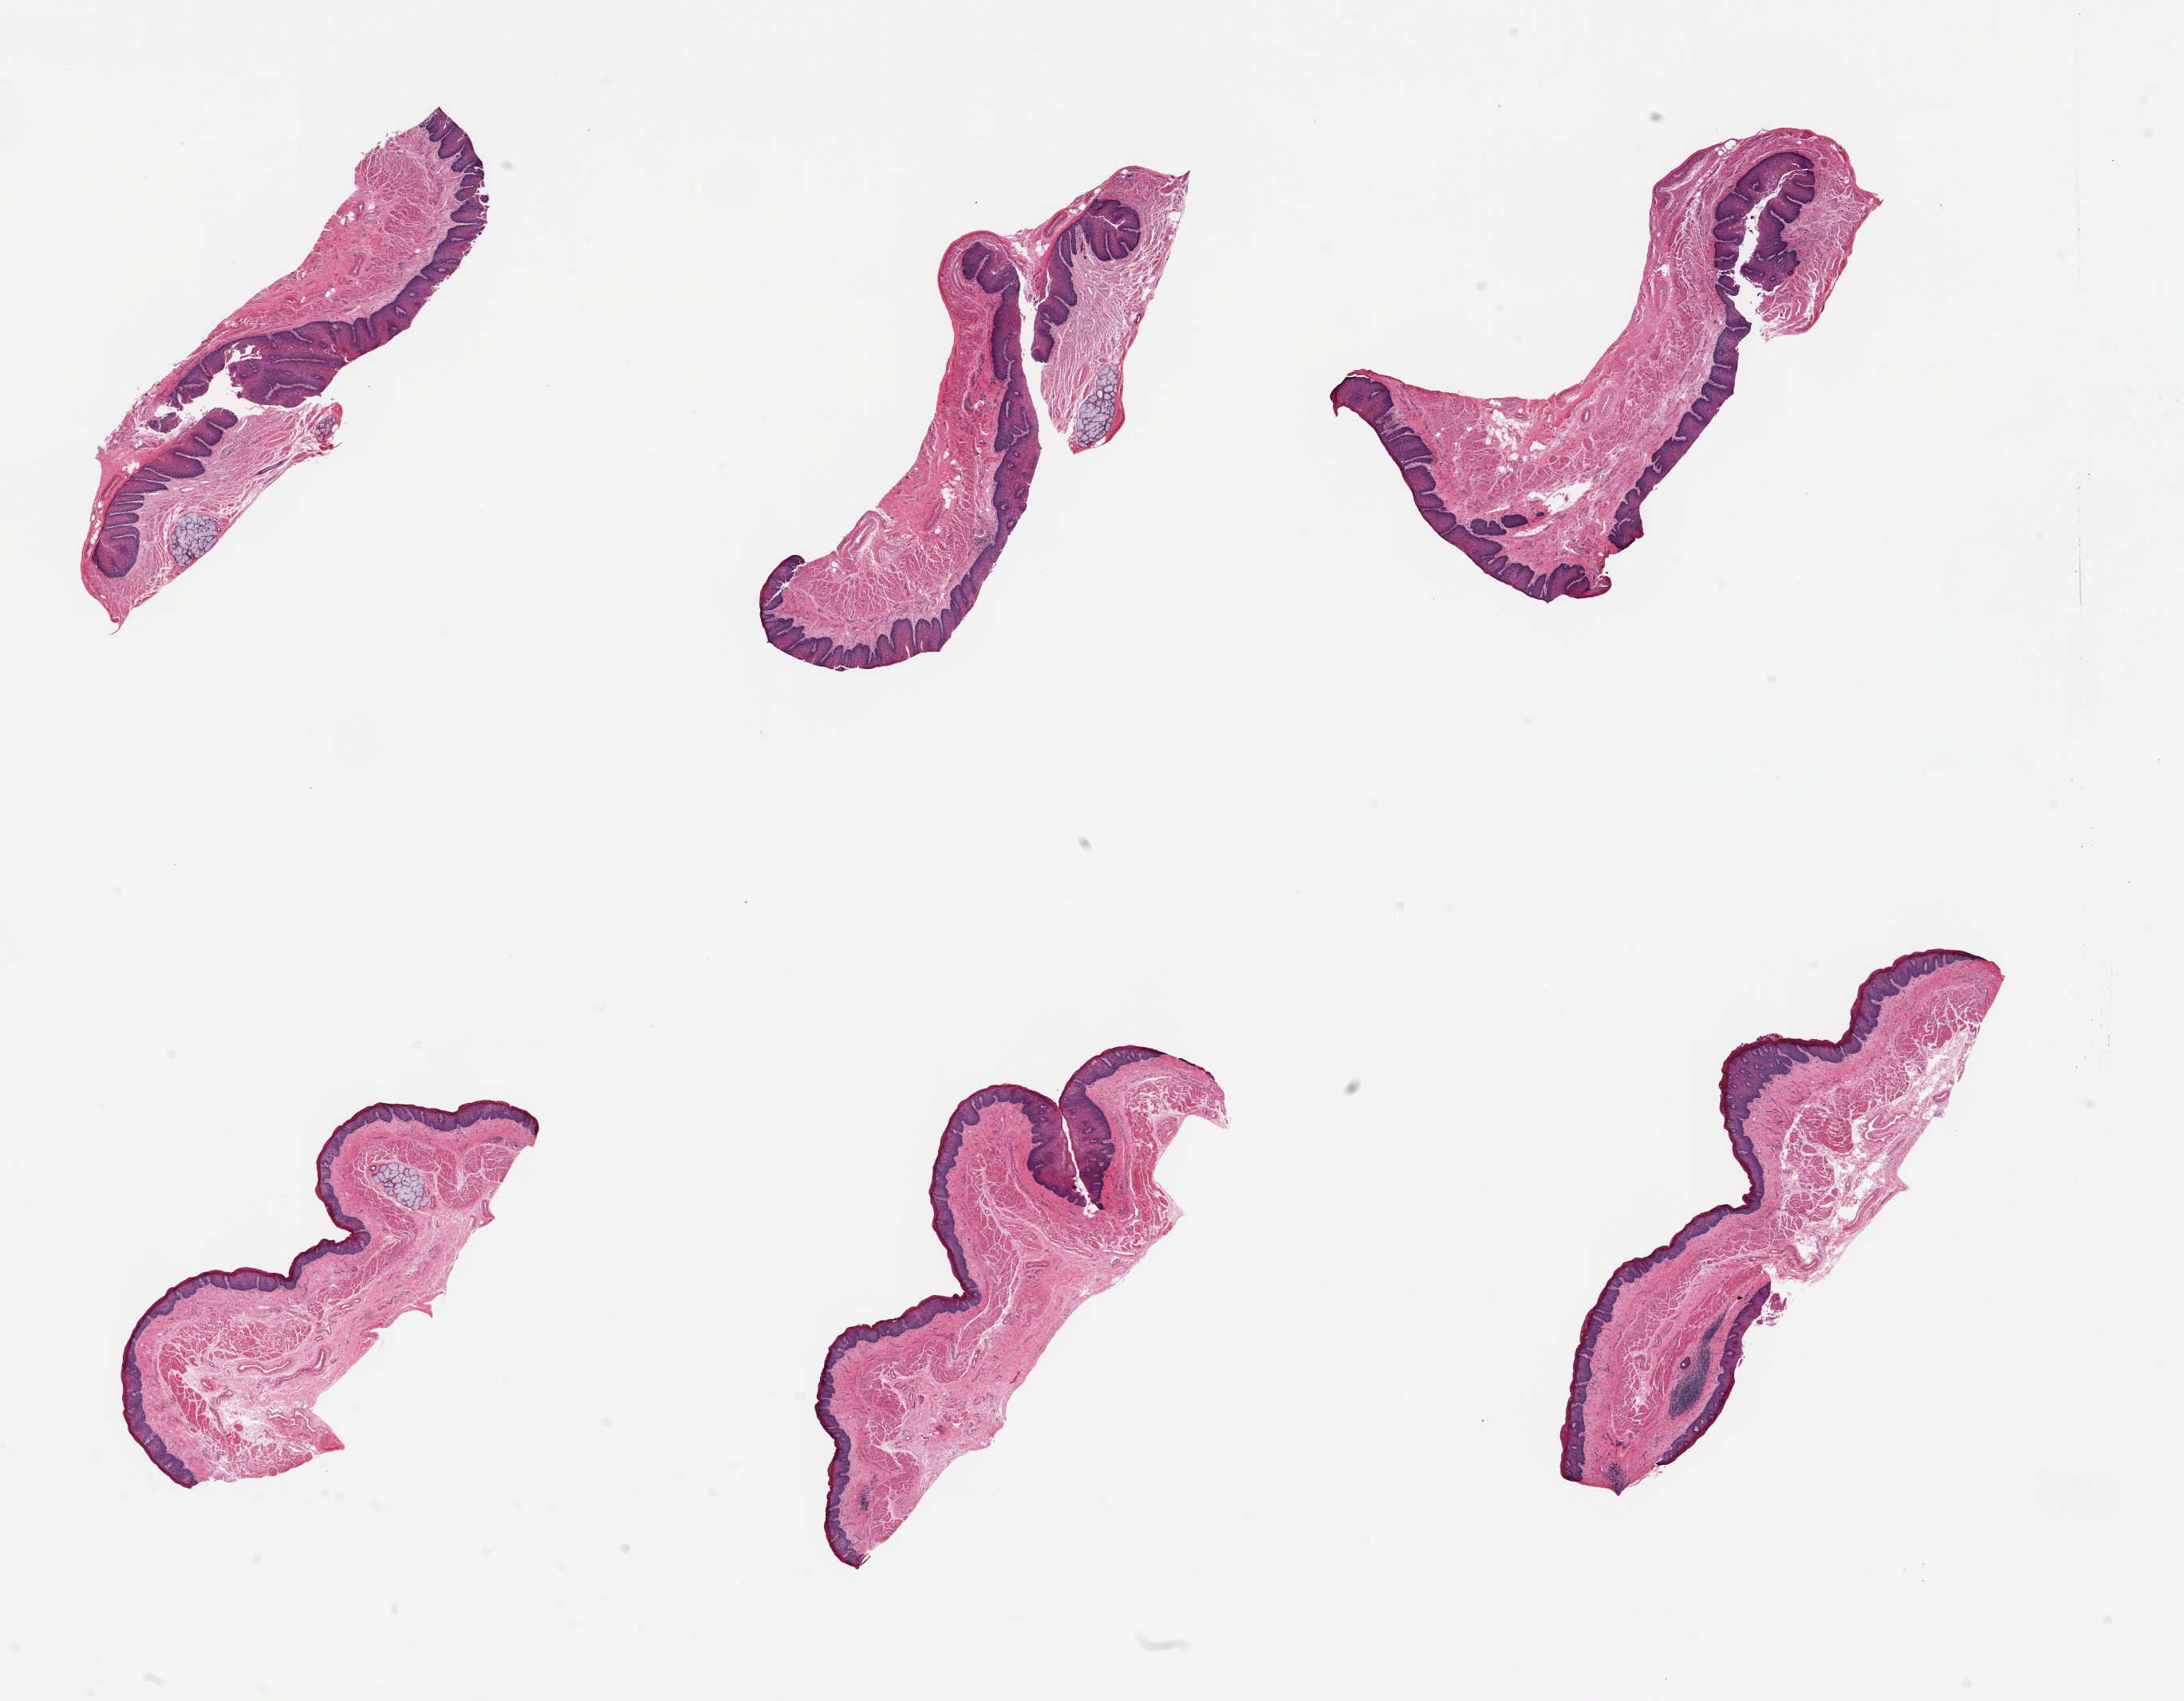
Whole-slide image, hematoxylin and eosin (H&E) stain, whole scanned area (about 21.7 x 16.9 mm) shown as a low-resolution overview. PAXgene-fixed, paraffin-embedded tissue. Target tissue: esophageal mucous membrane. Tissue donor sample.
Pathologist's review note for this sample: 6 pieces; ~ 207um squamous epithelium with parakeratosis; 3 pieces contain submucosal glands.